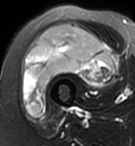
MRI of an extremity soft-tissue mass, one axial slice; slice 38 of 95 in the series (ordered by position); T2-weighted fat-saturated; MR volume resampled by the dataset authors to the PET/CT grid (not the native acquisition matrix); 3.27 mm slice thickness; 135 × 146 image matrix, field of view 132 × 143 mm. Female patient. From the clinical record (not read from this slice): histological type: pleiomorphic undifferentiated sarcoma; grade: high; site of the primary tumour: right quadricep.
Outlined on this slice (expert contour drawn on MRI and transferred to this co-registered scan by the dataset authors):
- gross tumour volume including surrounding oedema: bounding box [x1, y1, x2, y2] px = [23, 25, 118, 117]
- gross tumour volume (mass): [23, 25, 118, 117]